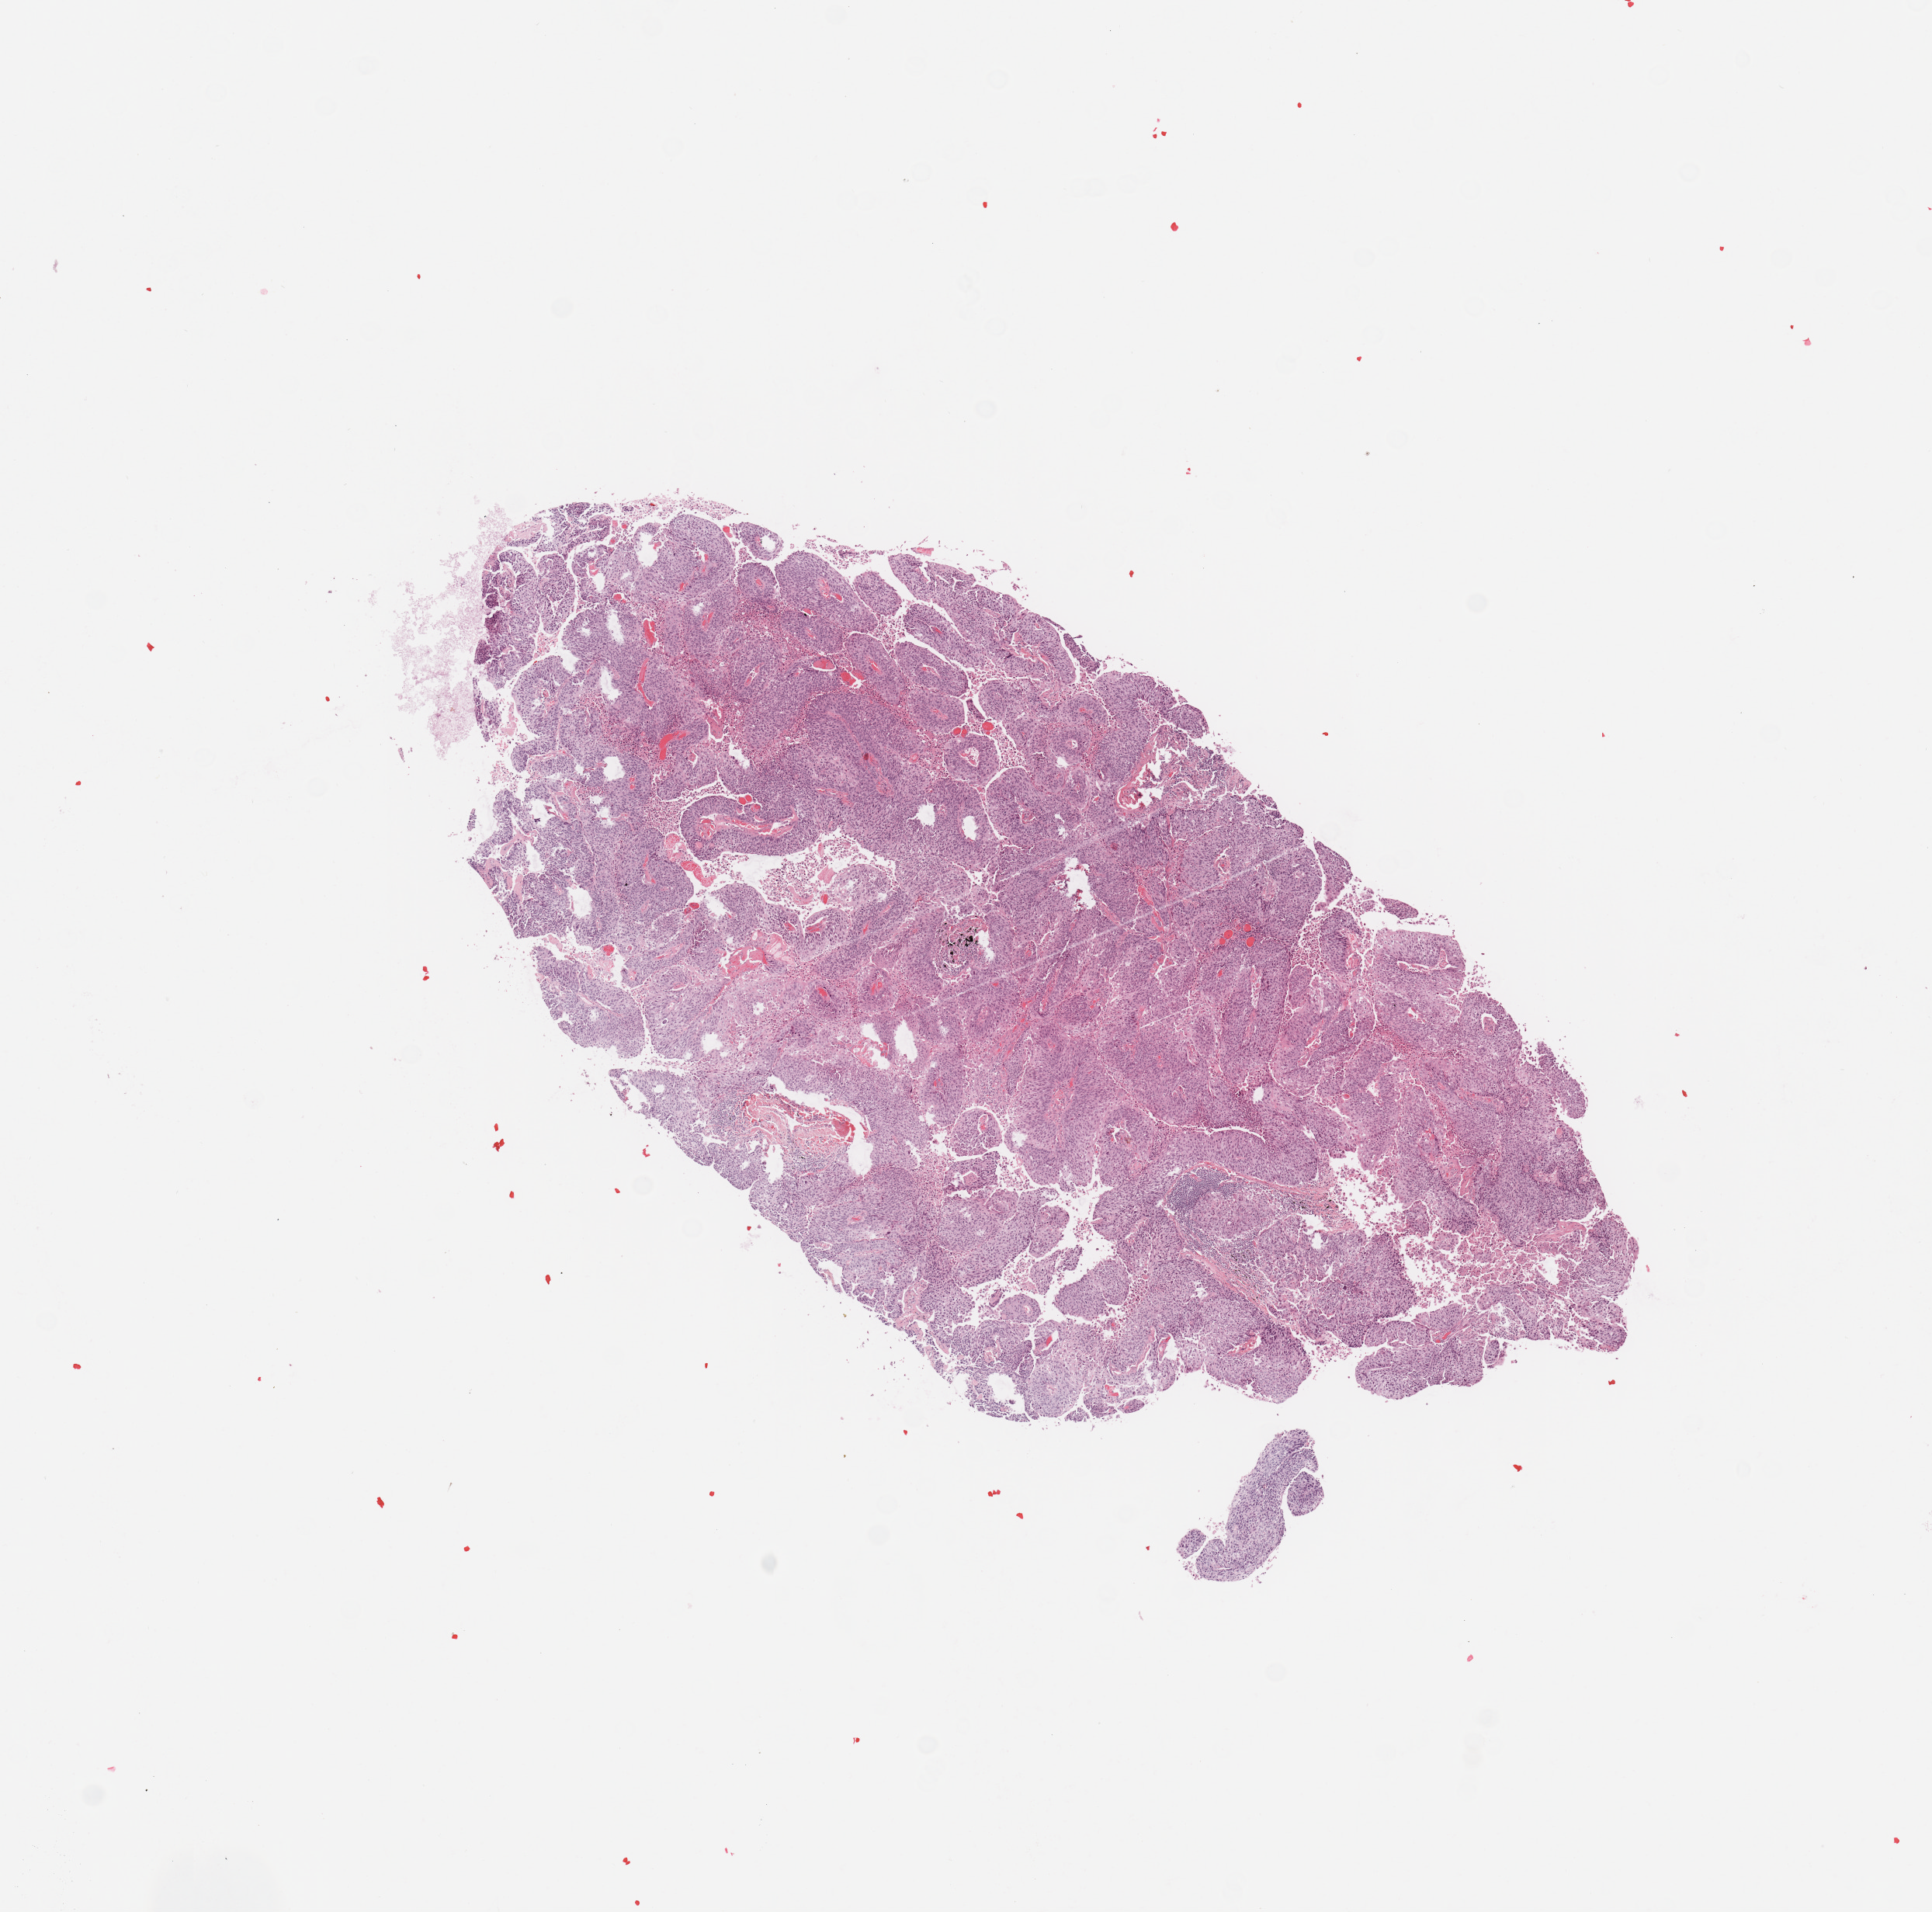
Whole-slide histology image, H&E — whole scanned area (about 9.8 x 9.7 mm, from a 20x scan) shown as a low-resolution overview, tumour tissue sample, sampled site: lung. 68-year-old male patient. Histologic grade: G3 (poorly differentiated). Slide review estimates, as recorded: tumour nuclei 85%, necrosis 5%.
* histologic diagnosis: Squamous cell carcinoma, NOS
* primary tumour site (as recorded): left upper lobe
* AJCC pathologic stage: IIB